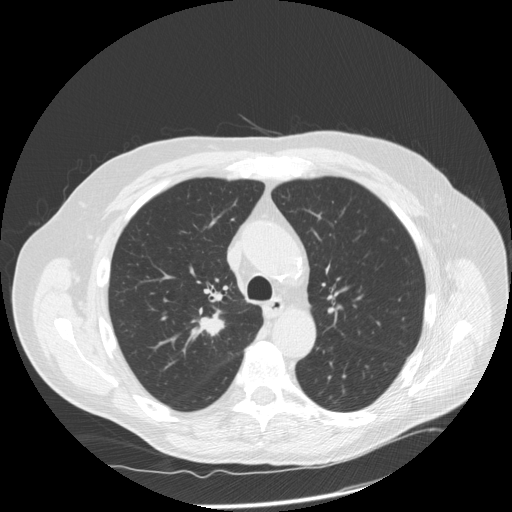
Low-dose screening chest CT, one axial slice. Reconstruction kernel STANDARD. 120 kVp. Lung window (W 1500 / L -600 HU). 2.5 mm slice thickness. 512 × 512 image matrix, field of view 390 × 390 mm.
Outlined on this slice (manually delineated by an expert):
- lesion 1 (tumor, upper lobe of right lung): box from (x=200, y=315) to (x=223, y=335) px